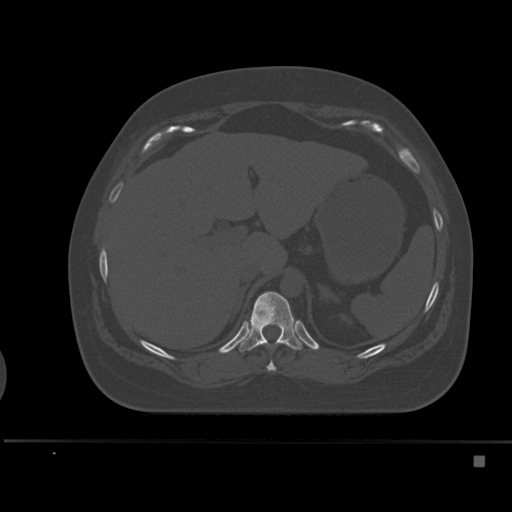
CT including the spine, one axial slice. Position 235 of 495 along the scan axis. Bone window (W 1800 / L 400 HU). 1.5 mm slice thickness. 512 × 512 image matrix, field of view 404 × 404 mm. Patient: female, 33 years. Case-level facts recorded for this patient, not image findings: primary cancer: breast; vertebrae with lytic lesions (as recorded): T1.
Outlined on this slice (semi-automatic segmentation, software-assisted and operator-edited):
- T10 vertebra: bounding box (x1, y1, x2, y2) in pixels: (267, 343, 276, 371)
- T11 vertebra: (236, 291, 307, 352)